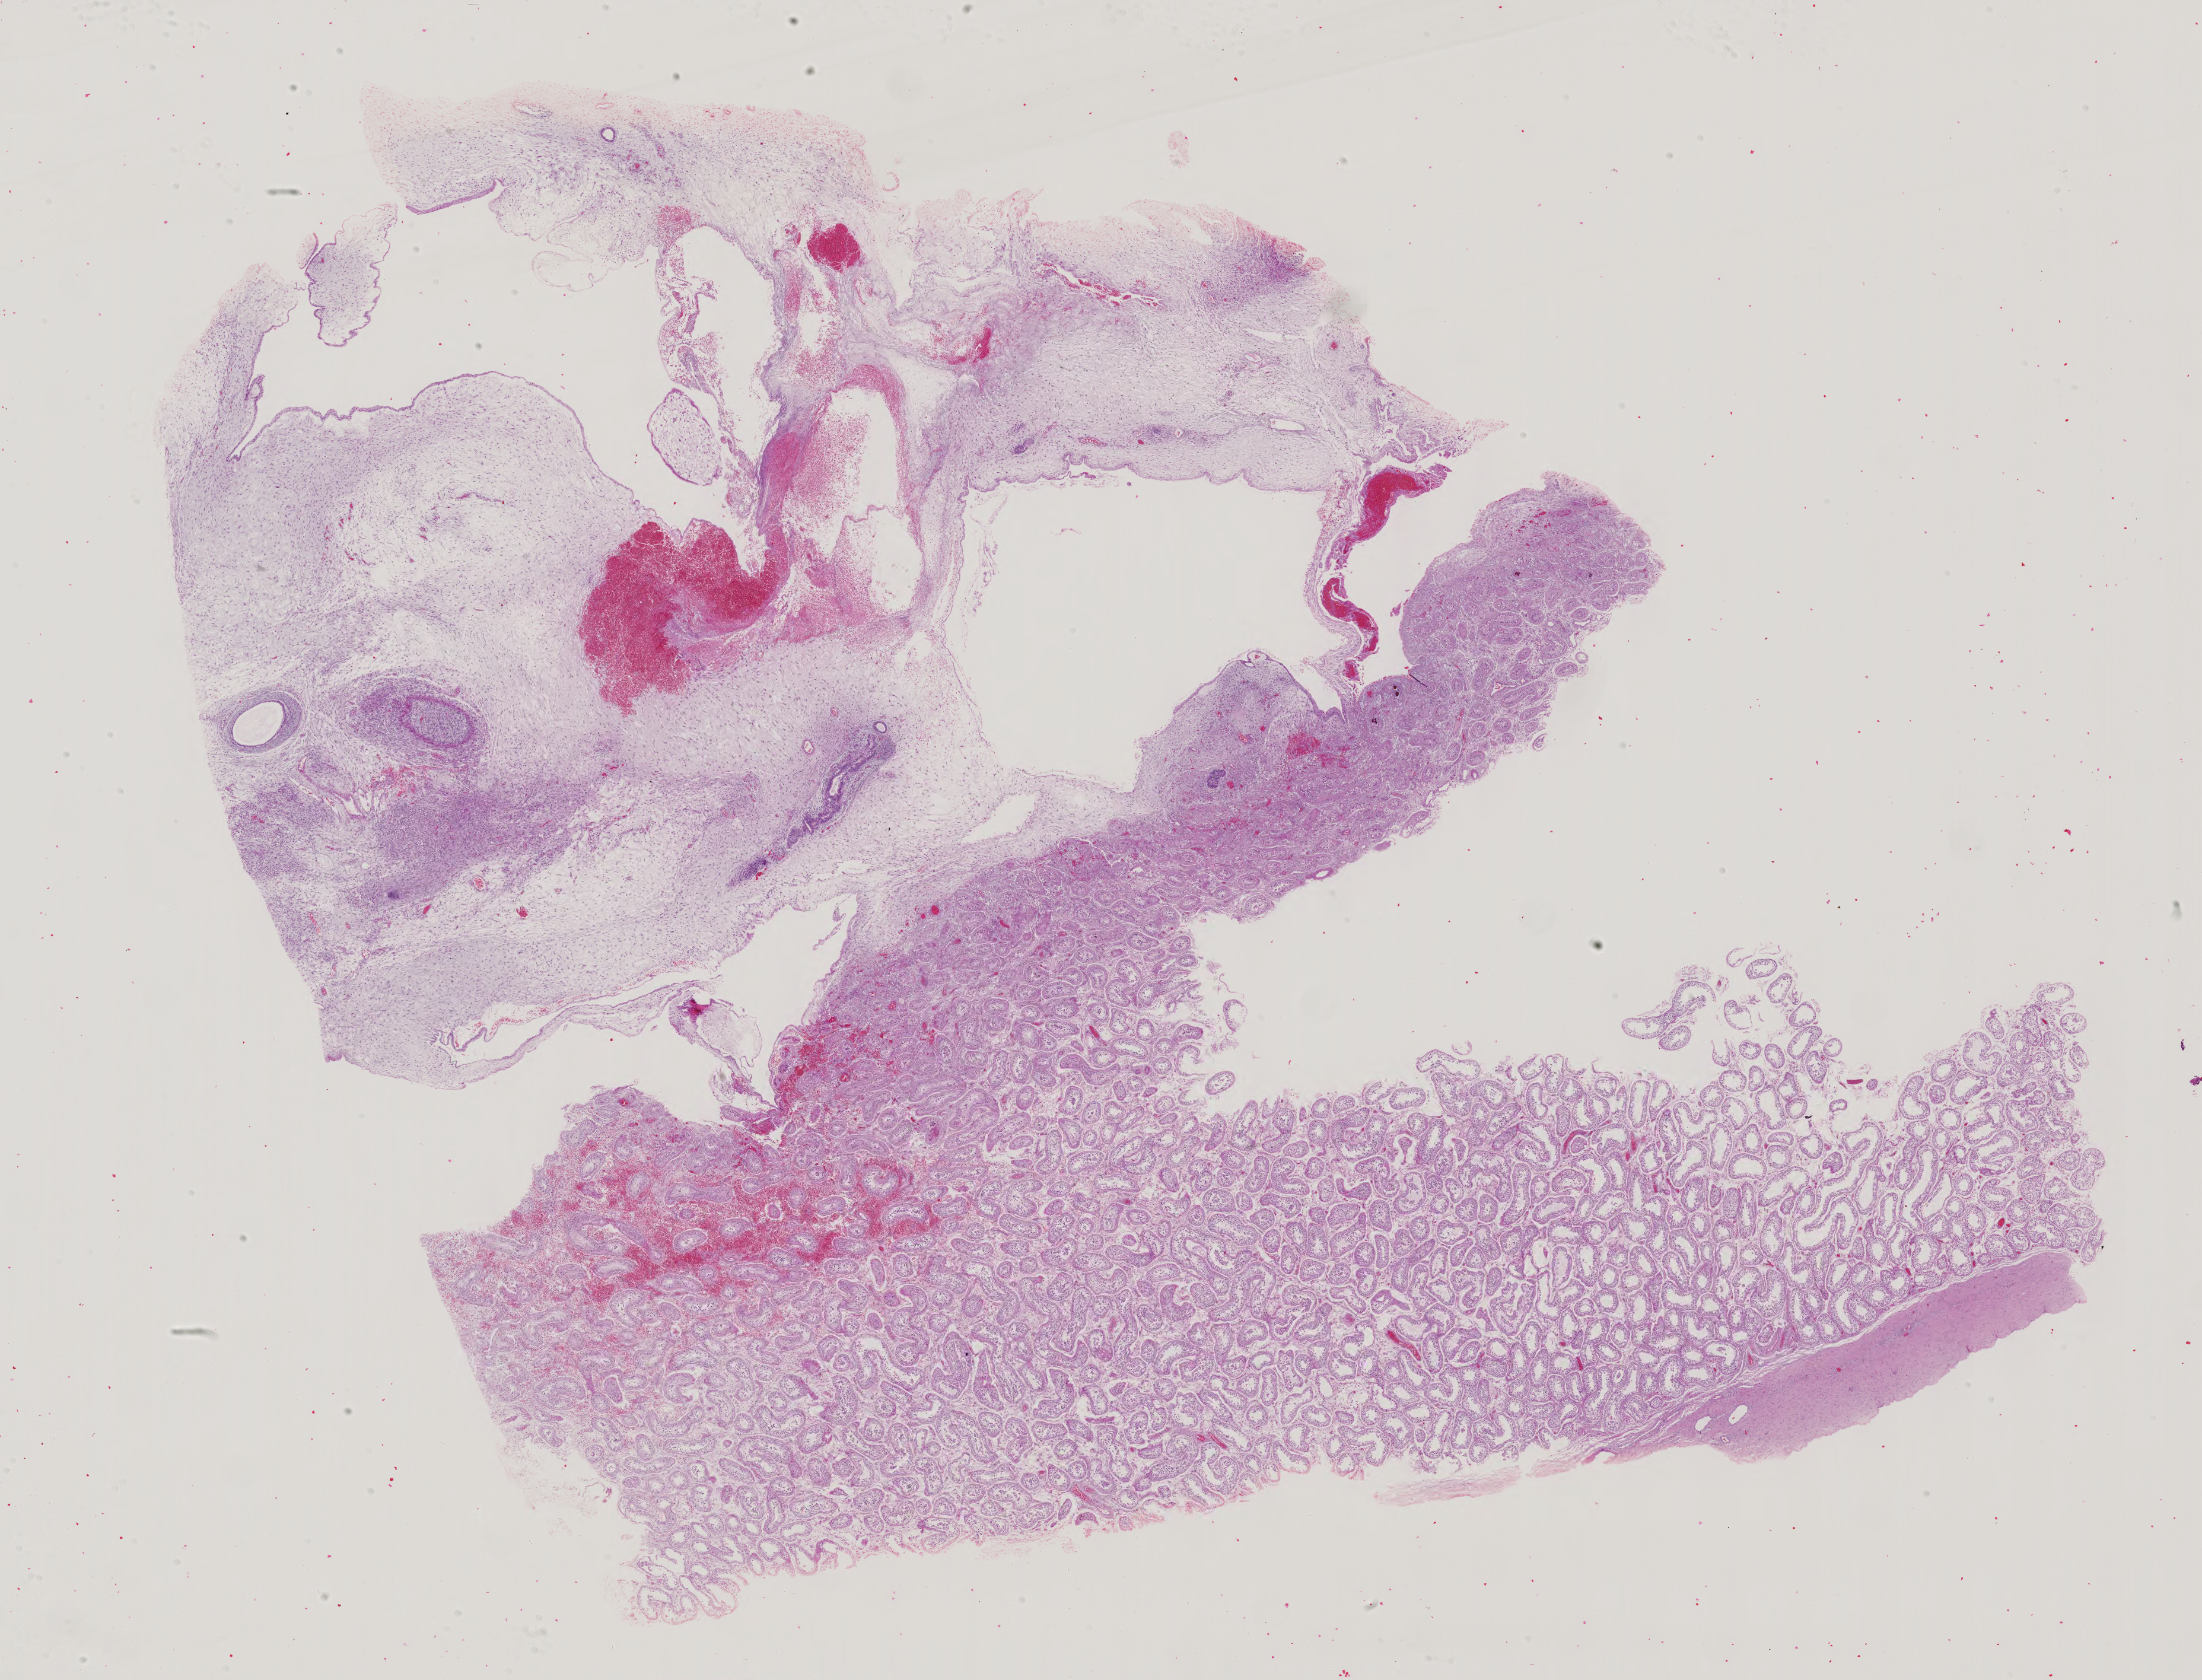
Whole-slide histology image, H&E, whole scanned area (about 27.0 x 20.6 mm, from a 40x scan) shown as a low-resolution overview. Male patient.
Specimen: FFPE section; primary tumour sample from the testis.